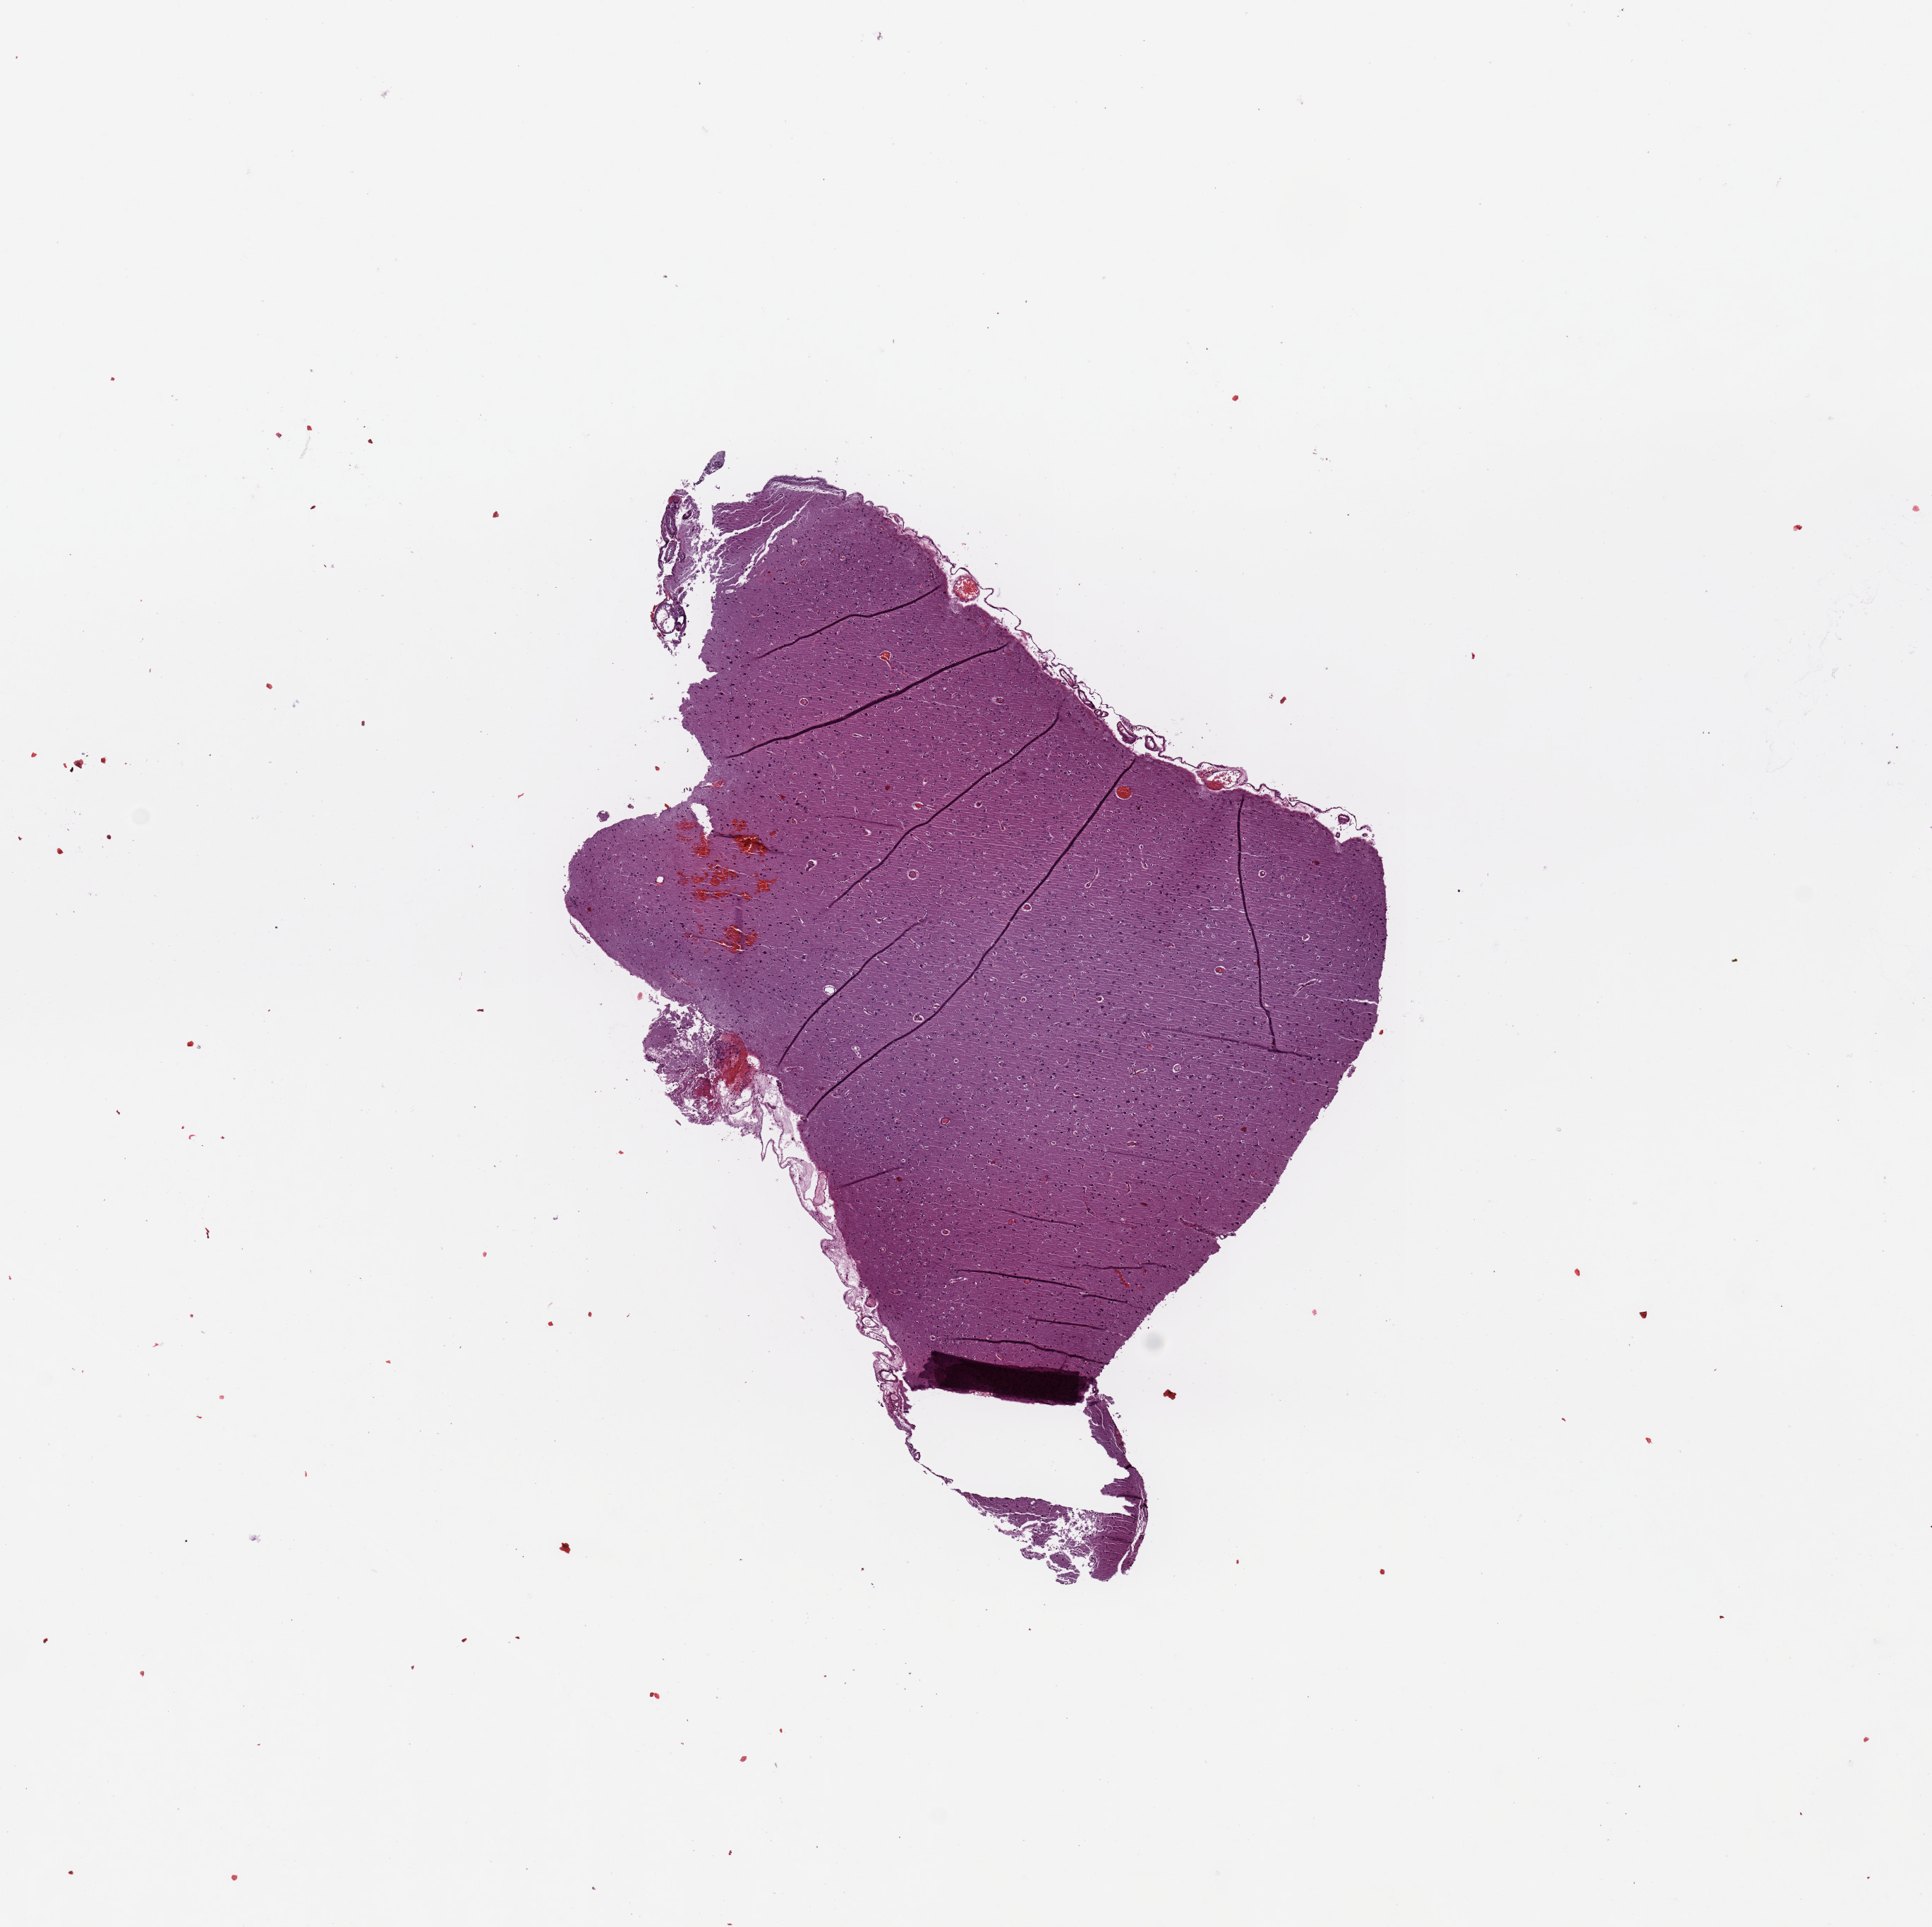
Digitized H&E tissue section (whole slide) — low-resolution overview of the scanned area, about 10.8 x 10.8 mm (slide scanned at 20x). Tumour tissue sample, brain. Patient: male, age 69 years.
Histologic diagnosis: Glioblastoma.